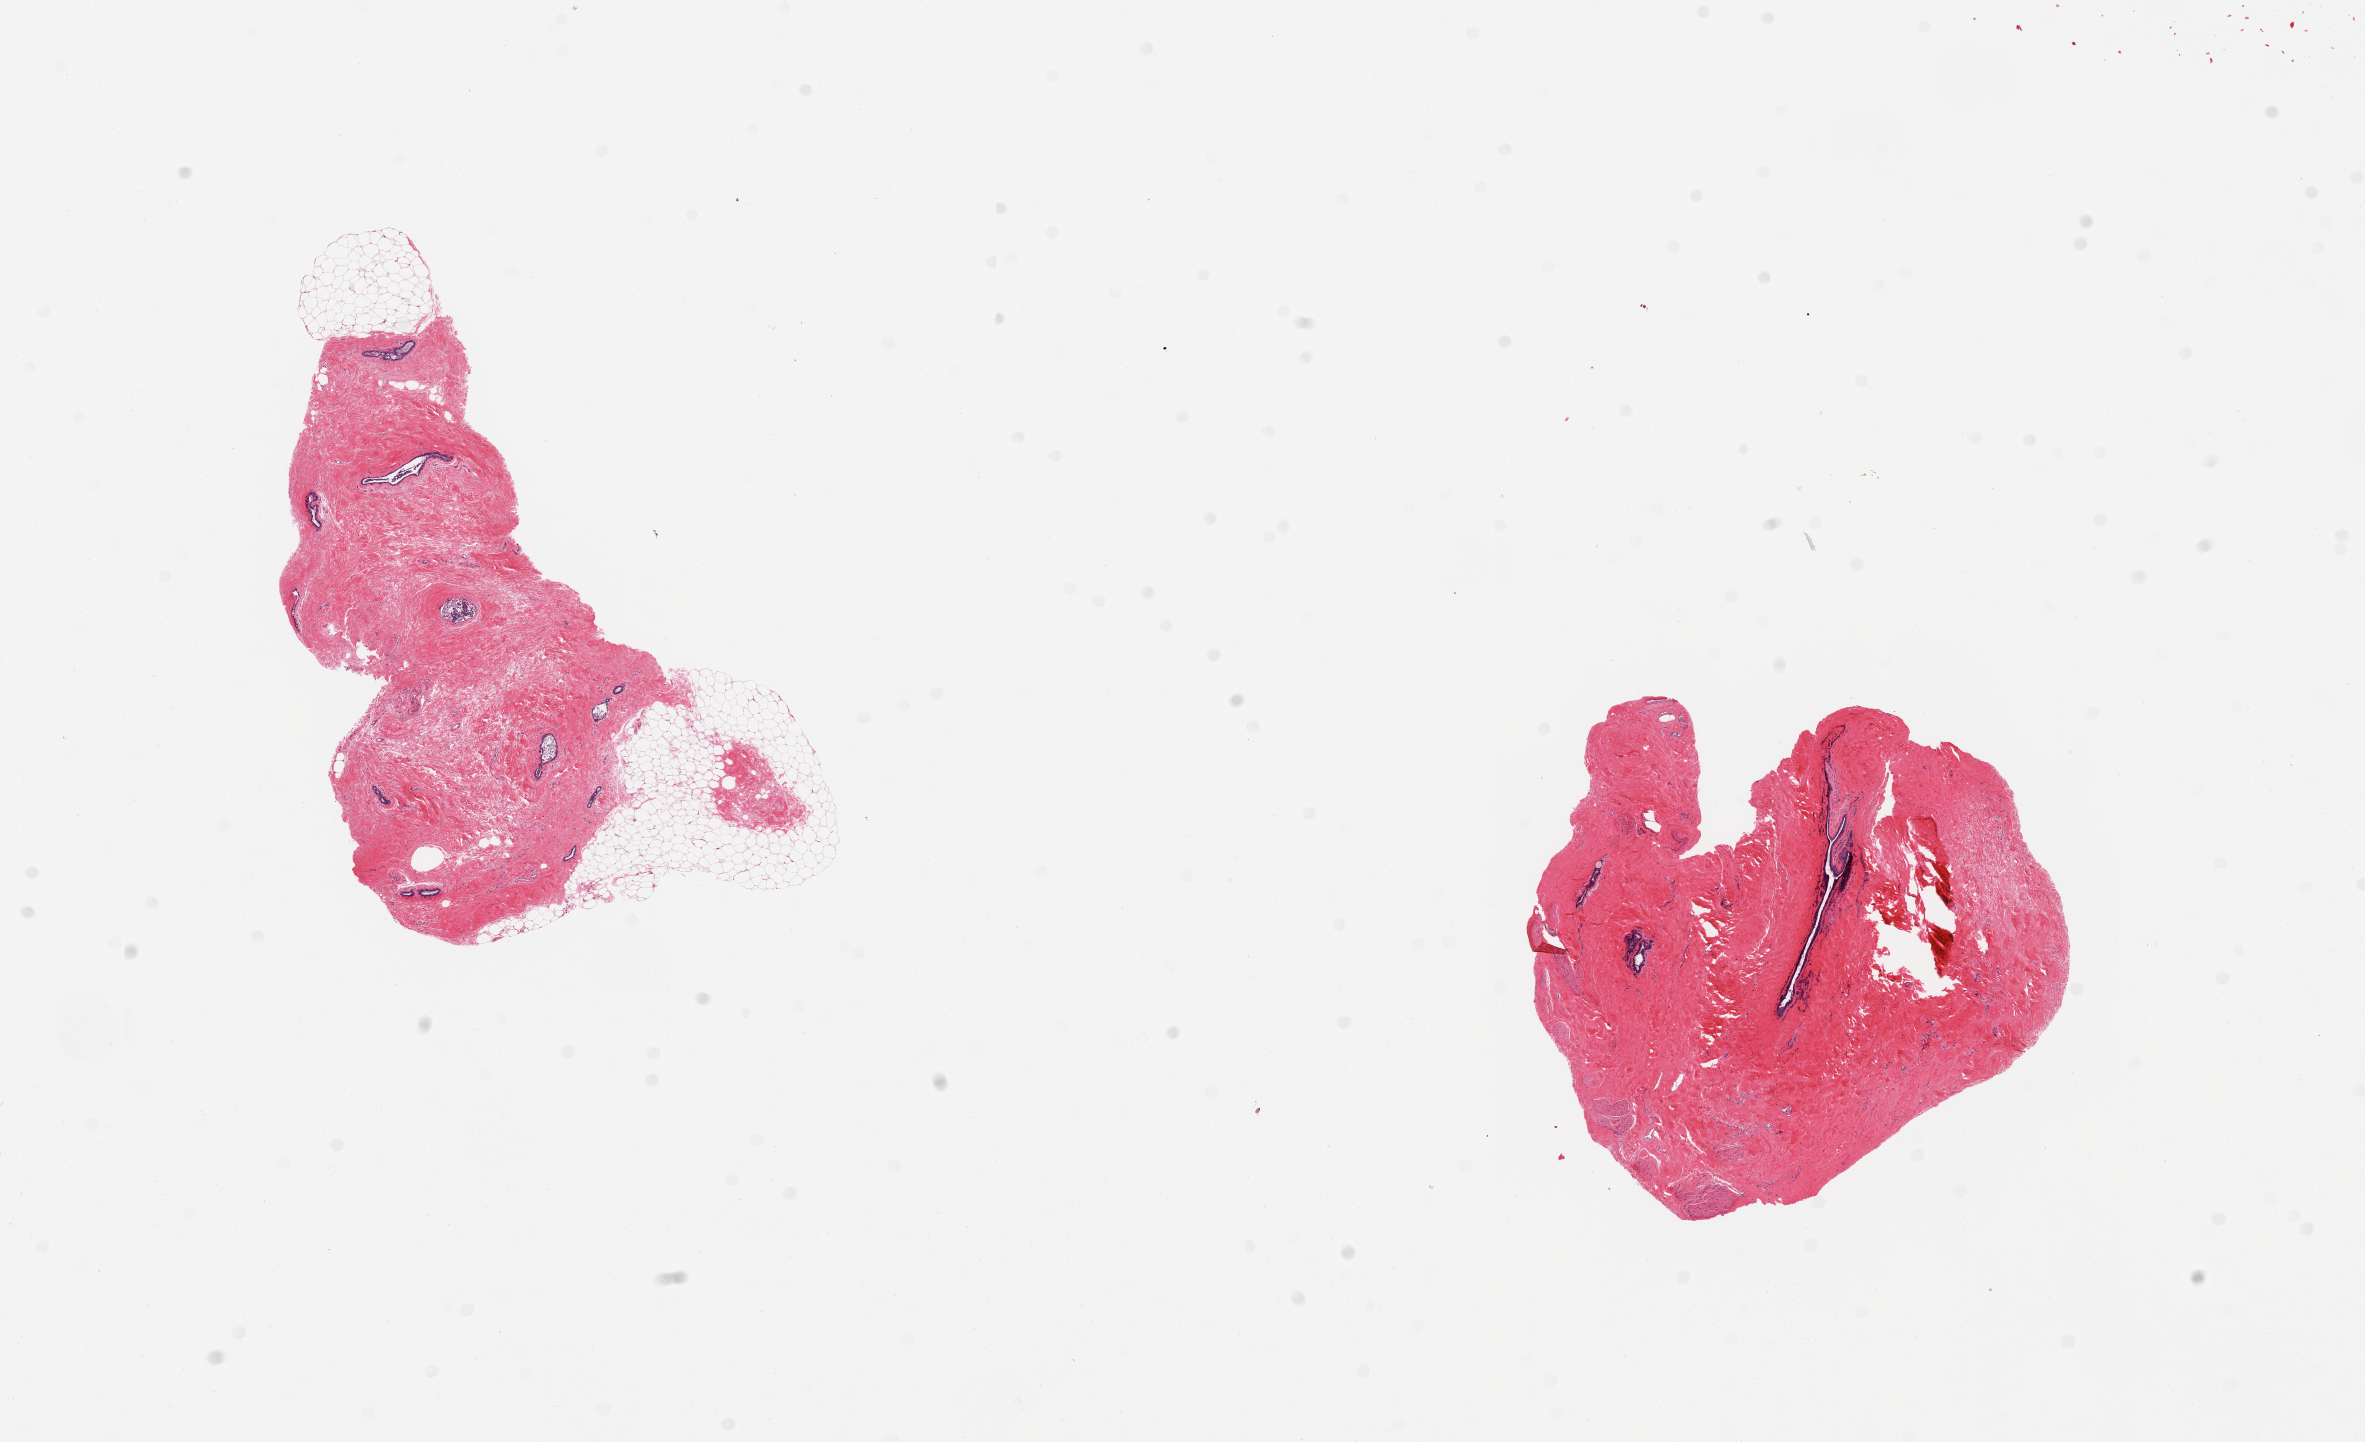
Digitized hematoxylin and eosin (H&E)-stained section — whole scanned area (about 18.7 x 11.4 mm, acquisition: 20x scan) shown as a low-resolution overview, PAXgene-fixed paraffin-embedded (PFPE) section, sampled site (target tissue): breast, tissue donor sample.
* pathologist's review note for this sample: 2 pieces, gynecomastoid stromal hyperplasia; ductal elements